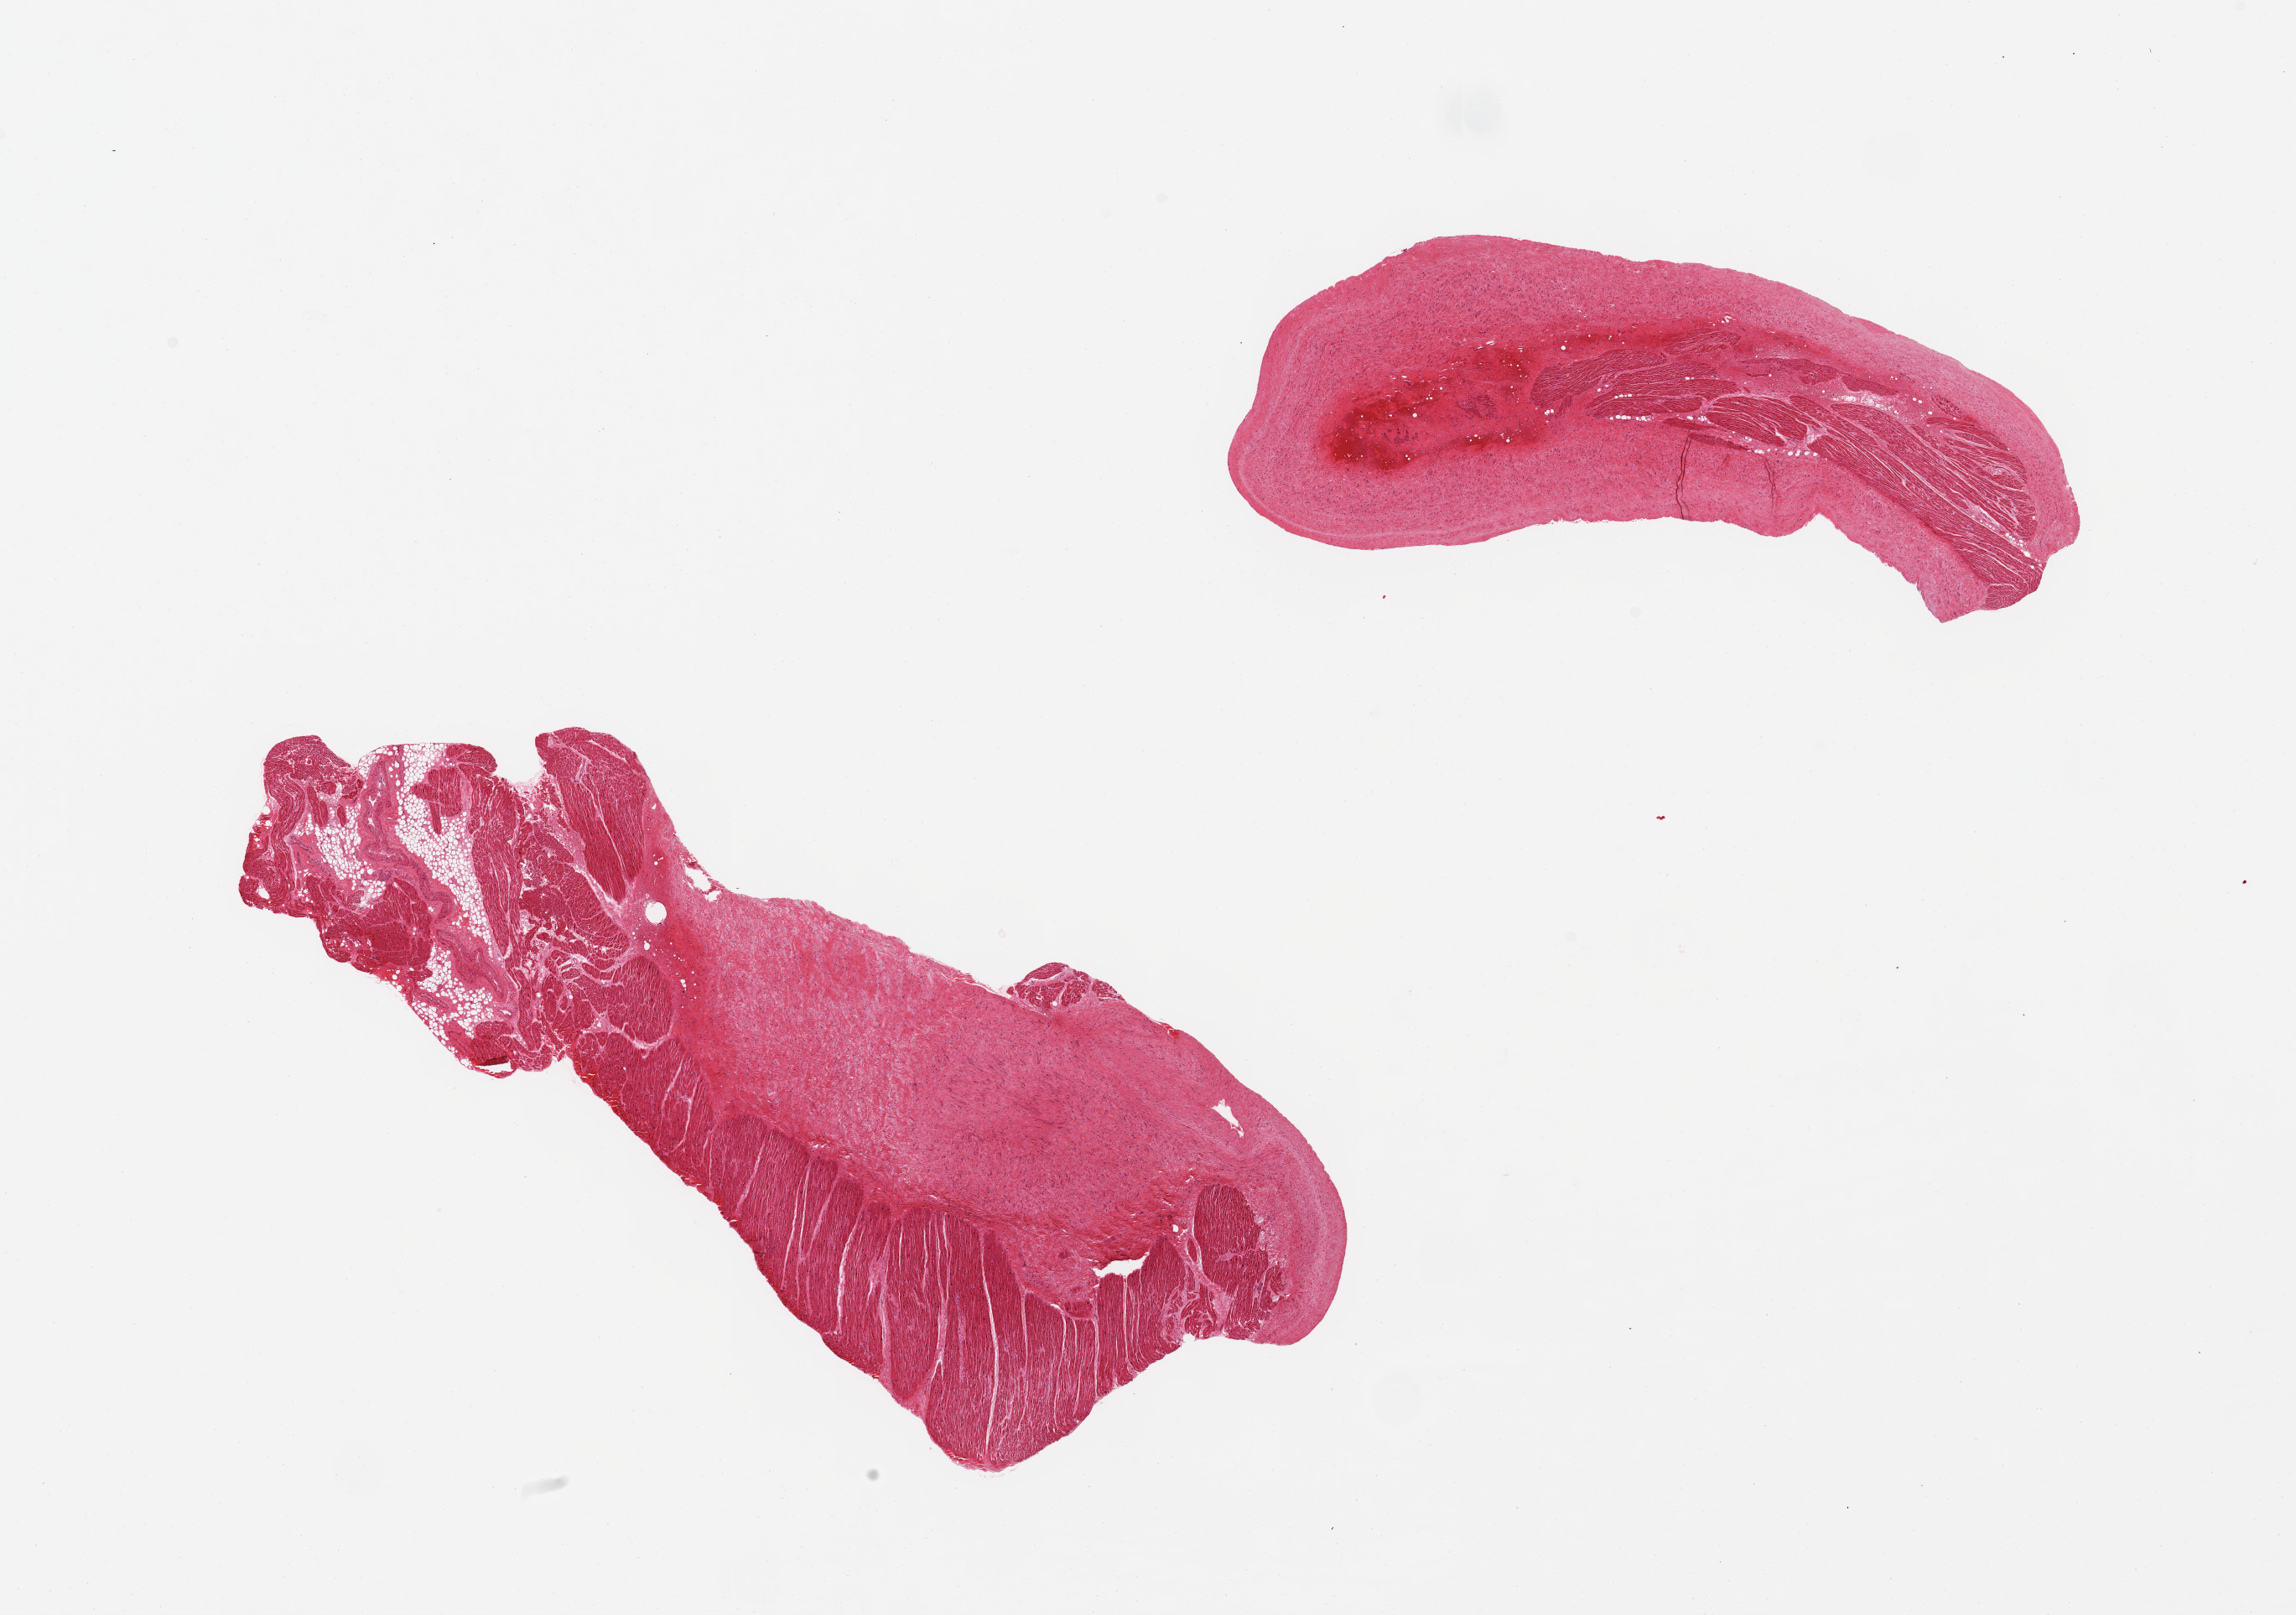
Digitized H&E-stained section — a low-resolution overview of the entire scanned area, about 21.7 x 15.2 mm (acquisition: 20x scan); PAXgene-fixed paraffin-embedded (PFPE) section; target tissue: auricular appendage; donor tissue sample. Male donor.
Review note (as recorded): 2 pieces; ~50% is fibrous/fatty.